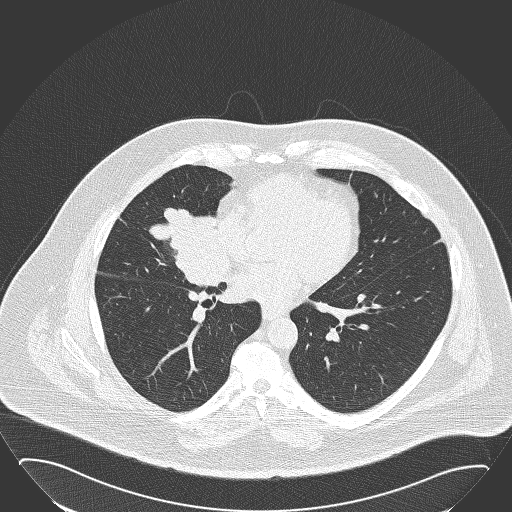
Low-dose screening chest CT, one axial slice; reconstruction kernel B50f; lung window (W 1500 / L -600 HU); 2 mm slice thickness; 512 × 512 image matrix, field of view 432 × 432 mm.
Structures marked on this image (expert manual segmentation):
- lesion 1 (tumor, hilum of right lung): bounding box [x1, y1, x2, y2] px = [150, 208, 227, 287]